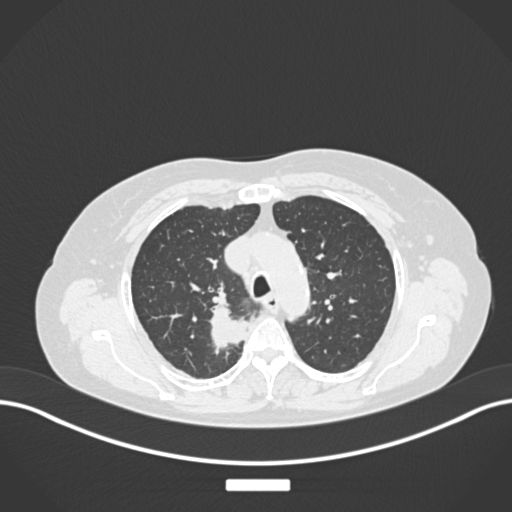
Chest CT, one axial slice; slice 190 of 237 in the series (ordered by position); 120 kVp; lung window (W 1500 / L -600 HU); 1 mm slice thickness; 512 × 512 image matrix, field of view 400 × 400 mm. Patient: female, 62 years. Case-level facts recorded for this patient, not image findings: clinical TNM (as recorded): T1c N1 M0.
Outlined on this slice (bounding box drawn by a radiologist):
- lung tumour (recorded histology: squamous cell carcinoma): bounding box <207,303,250,350> (left, top, right, bottom; pixels)